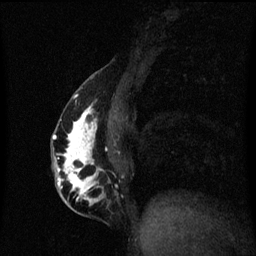
Breast MRI (dynamic contrast-enhanced), one sagittal slice; position 25 of 60 along the scan axis; dynamic contrast-enhanced series, image 2 of 3 at this slice position (ordered by acquisition); 1.5 T; TE 4.2 ms, TR 8.4 ms; 2 mm slice thickness; 256 × 256 image matrix, field of view 200 × 200 mm. Patient: female, 40 years.
Structures marked on this image (semi-automatically segmented with operator editing):
- analysis volume of interest (the breast-tissue region the enhancement analysis was run in; not a lesion): bounding box <52,84,117,211> (left, top, right, bottom; pixels)
- tumour enhancement mask (voxels above the 70 % enhancement threshold inside the analysis volume of interest): <53,104,102,203>